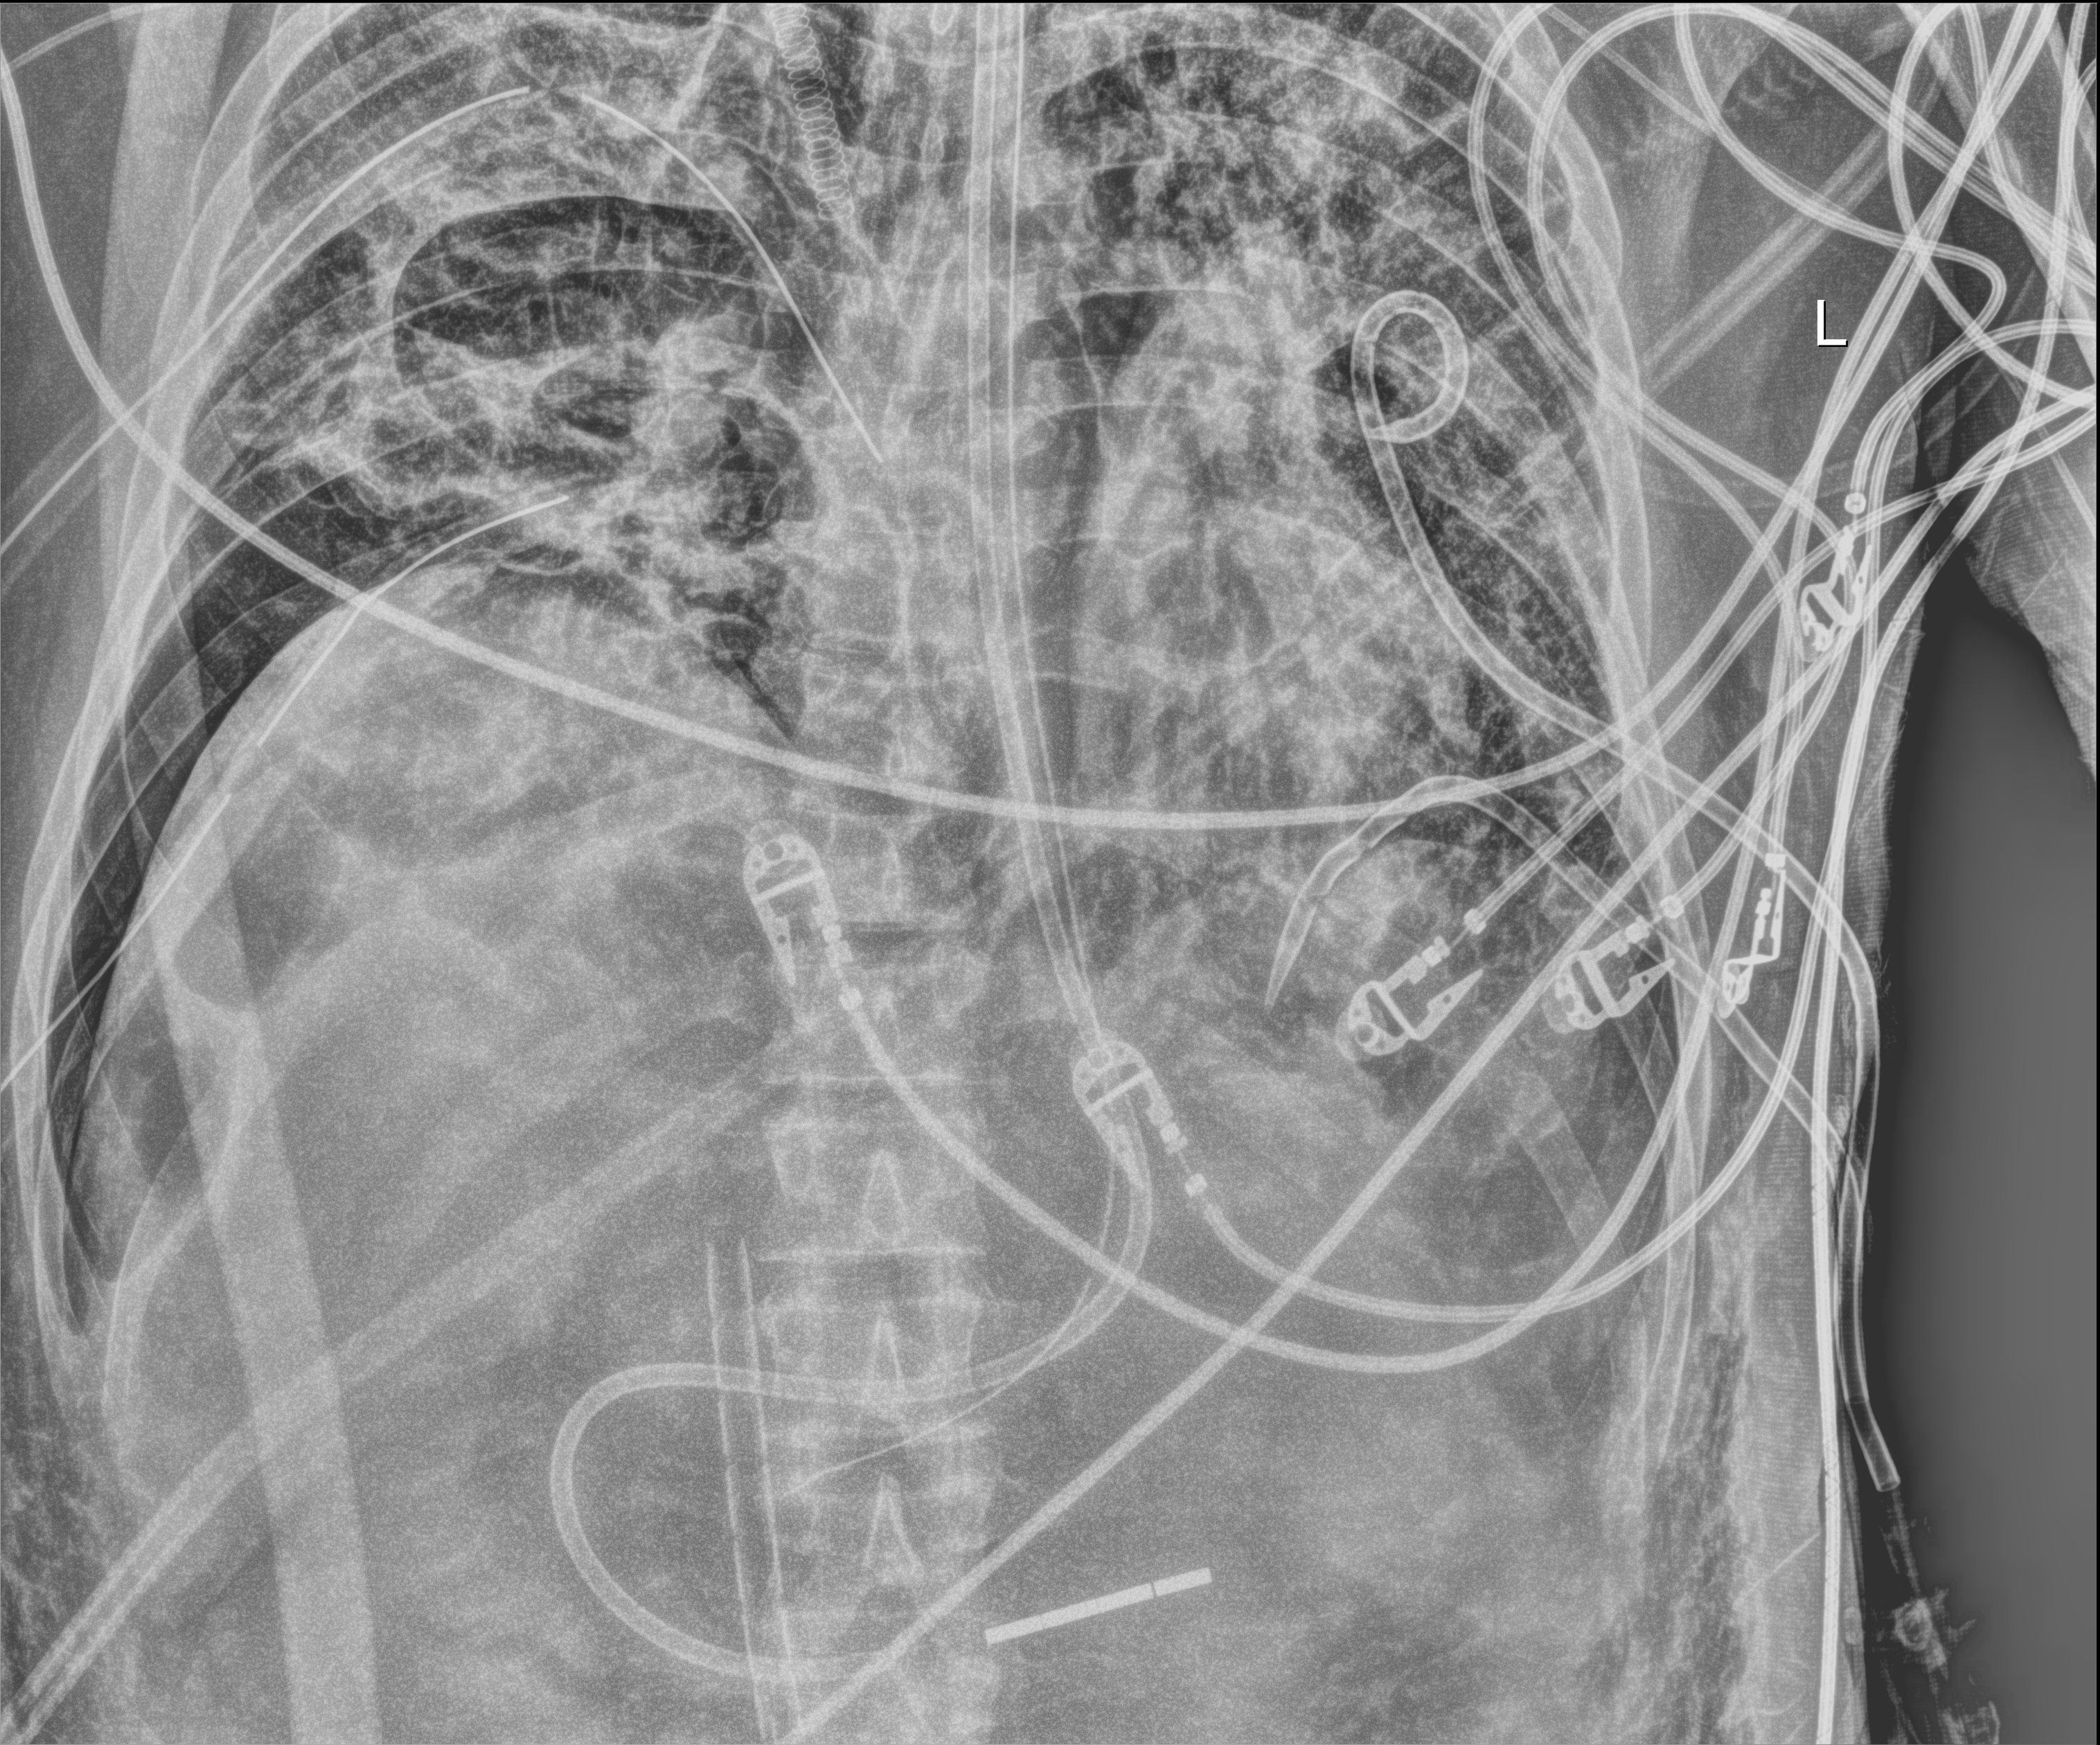
Chest X-ray; anteroposterior (AP) projection. Adult patient hospitalised with COVID-19, age 18–59 years.
From the hospital-stay record, not from the radiograph (when in the stay this image was taken is not recorded): chronic kidney disease (admission record): no; mechanically ventilated during this hospital stay: yes; admitted to intensive care during this hospital stay: yes.